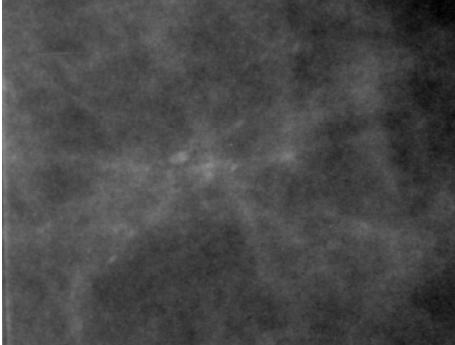
Region of interest cut from a scanned film mammogram (one marked finding), right breast, CC view, BI-RADS breast density category 2 (scale 1–4).
Marked abnormality: calcifications, morphology pleomorphic, distribution linear; BI-RADS assessment category 4; pathology (as recorded): malignant.